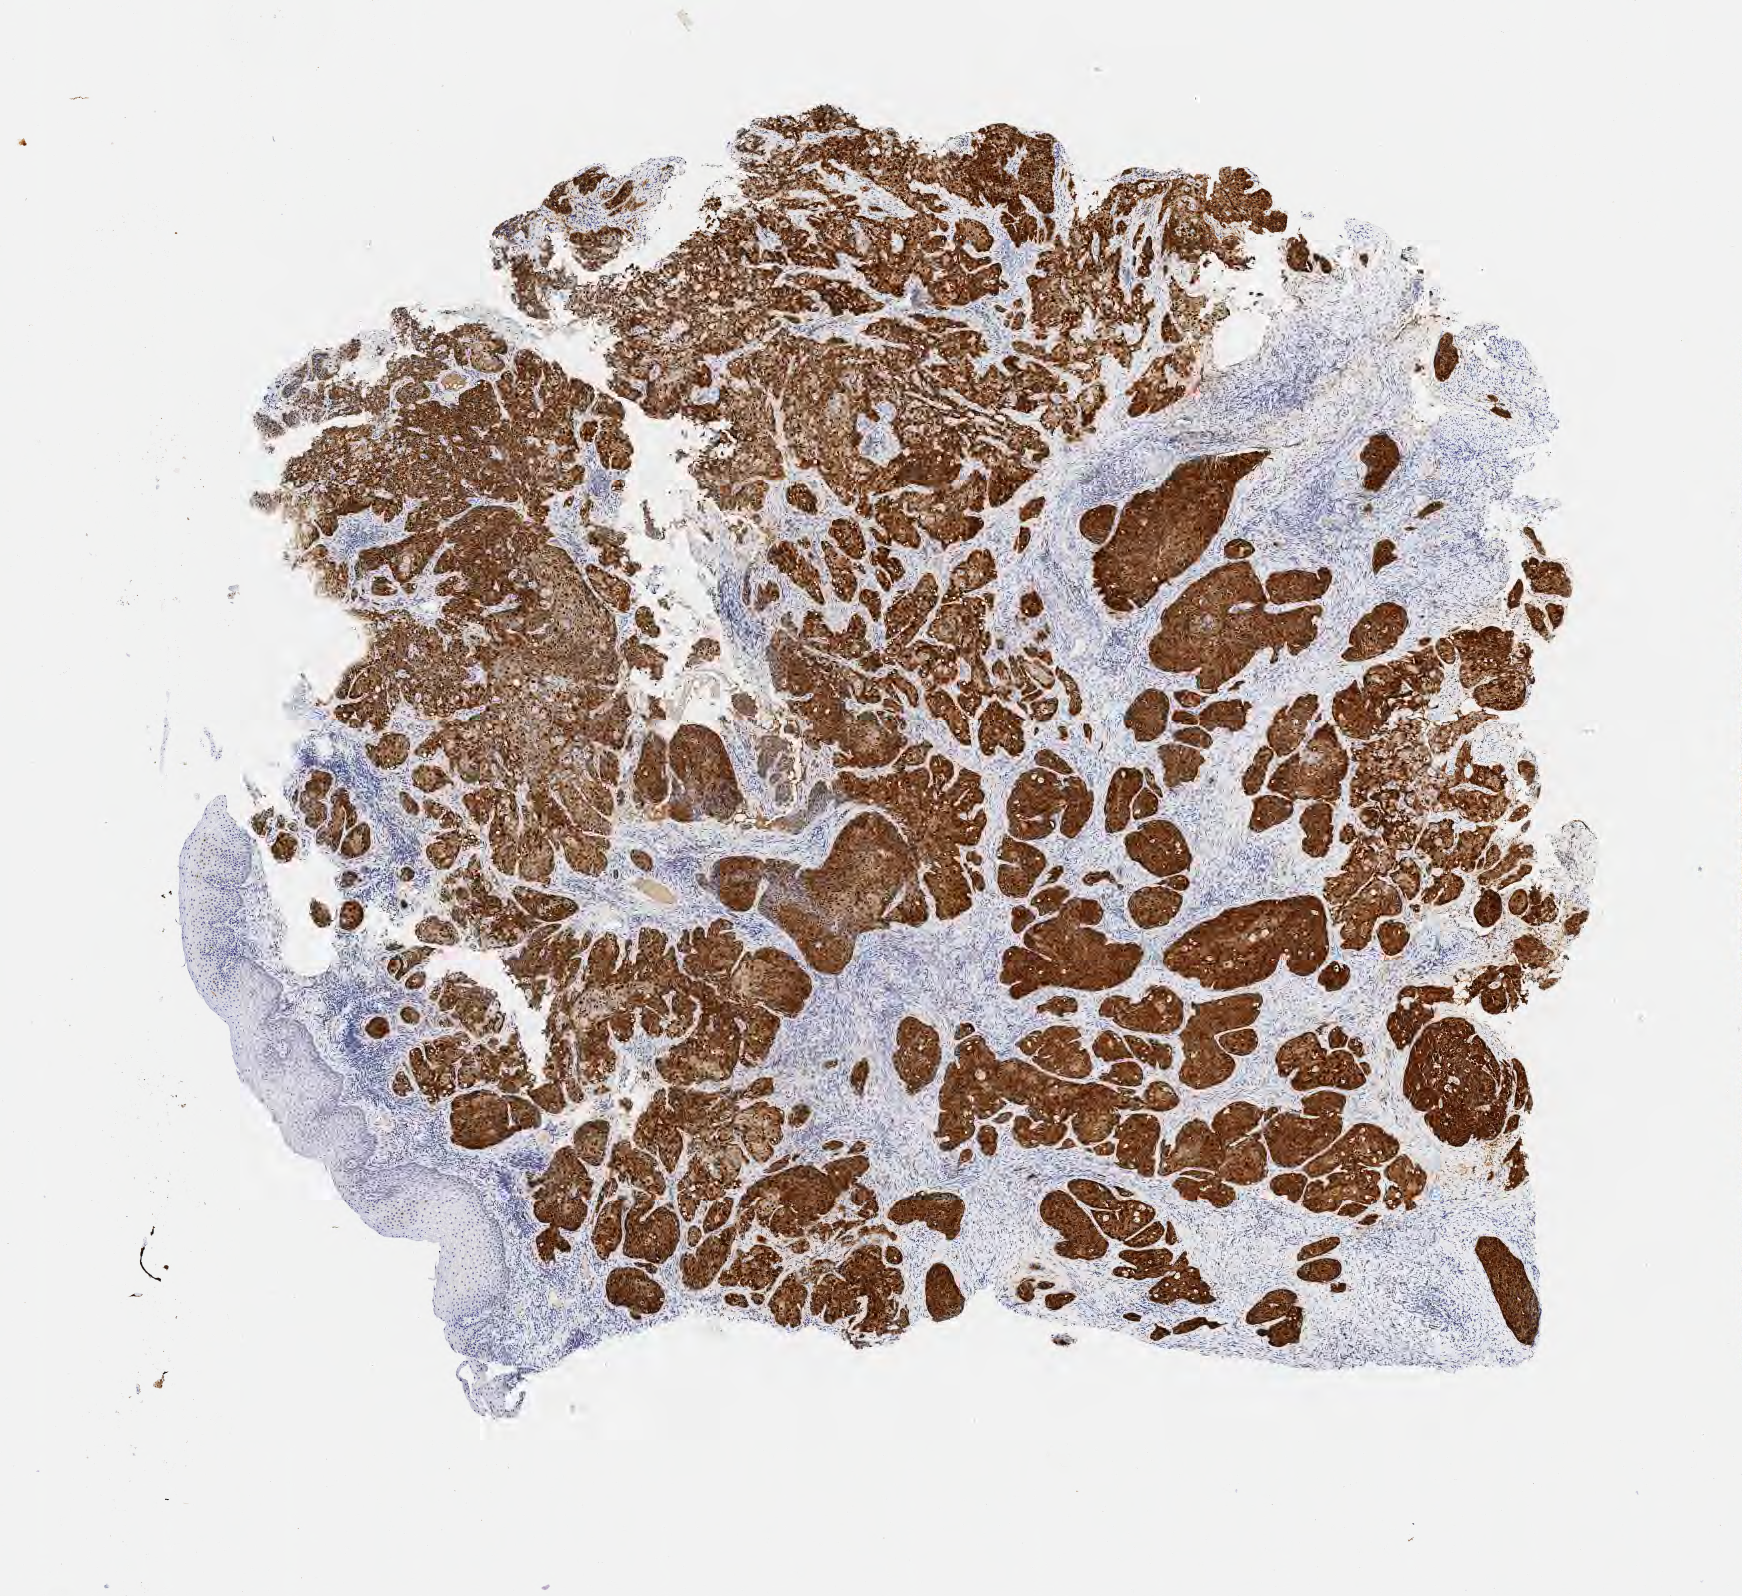
IHC for p16 (p16INK4a), whole-slide image, shown as a low-resolution overview of the whole scanned area (about 7.0 x 6.5 mm); specimen: tumor tissue; site: cervix. Patient: female, age 47 years.
* histologic diagnosis: Squamous cell carcinoma, keratinizing, NOS